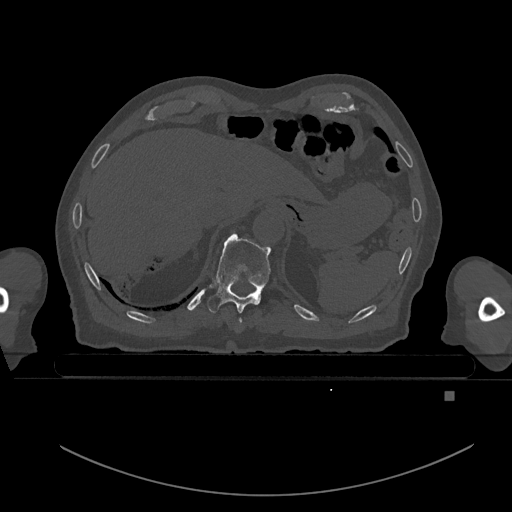
CT including the spine, one axial slice; position 88 of 969 along the scan axis; bone window (W 1800 / L 400 HU); 0.5 mm slice thickness; 512 × 512 image matrix, field of view 456 × 456 mm. Male patient, age 82 years. Case-level facts recorded for this patient, not image findings: primary cancer: prostate; vertebrae with lytic lesions (as recorded): T11, T9, T8, T2.
Annotated regions visible in this slice (semi-automatic segmentation, software-assisted and operator-edited):
- T10 vertebra: bounding box <207,234,271,313> (left, top, right, bottom; pixels)
- T9 vertebra: <239,318,242,324>